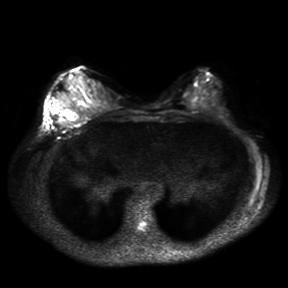
Breast MRI, one axial slice; slice 14 of 30 in the series (ordered by position); diffusion-weighted series; image 2 of 4 stored at this slice position (different b-values; order by instance number); 3 T; 288 × 288 image matrix, field of view 360 × 360 mm. Female patient.
Annotated regions visible in this slice (expert manual segmentation):
- tumour on diffusion-weighted imaging: bounding box <55,106,79,125> (left, top, right, bottom; pixels)